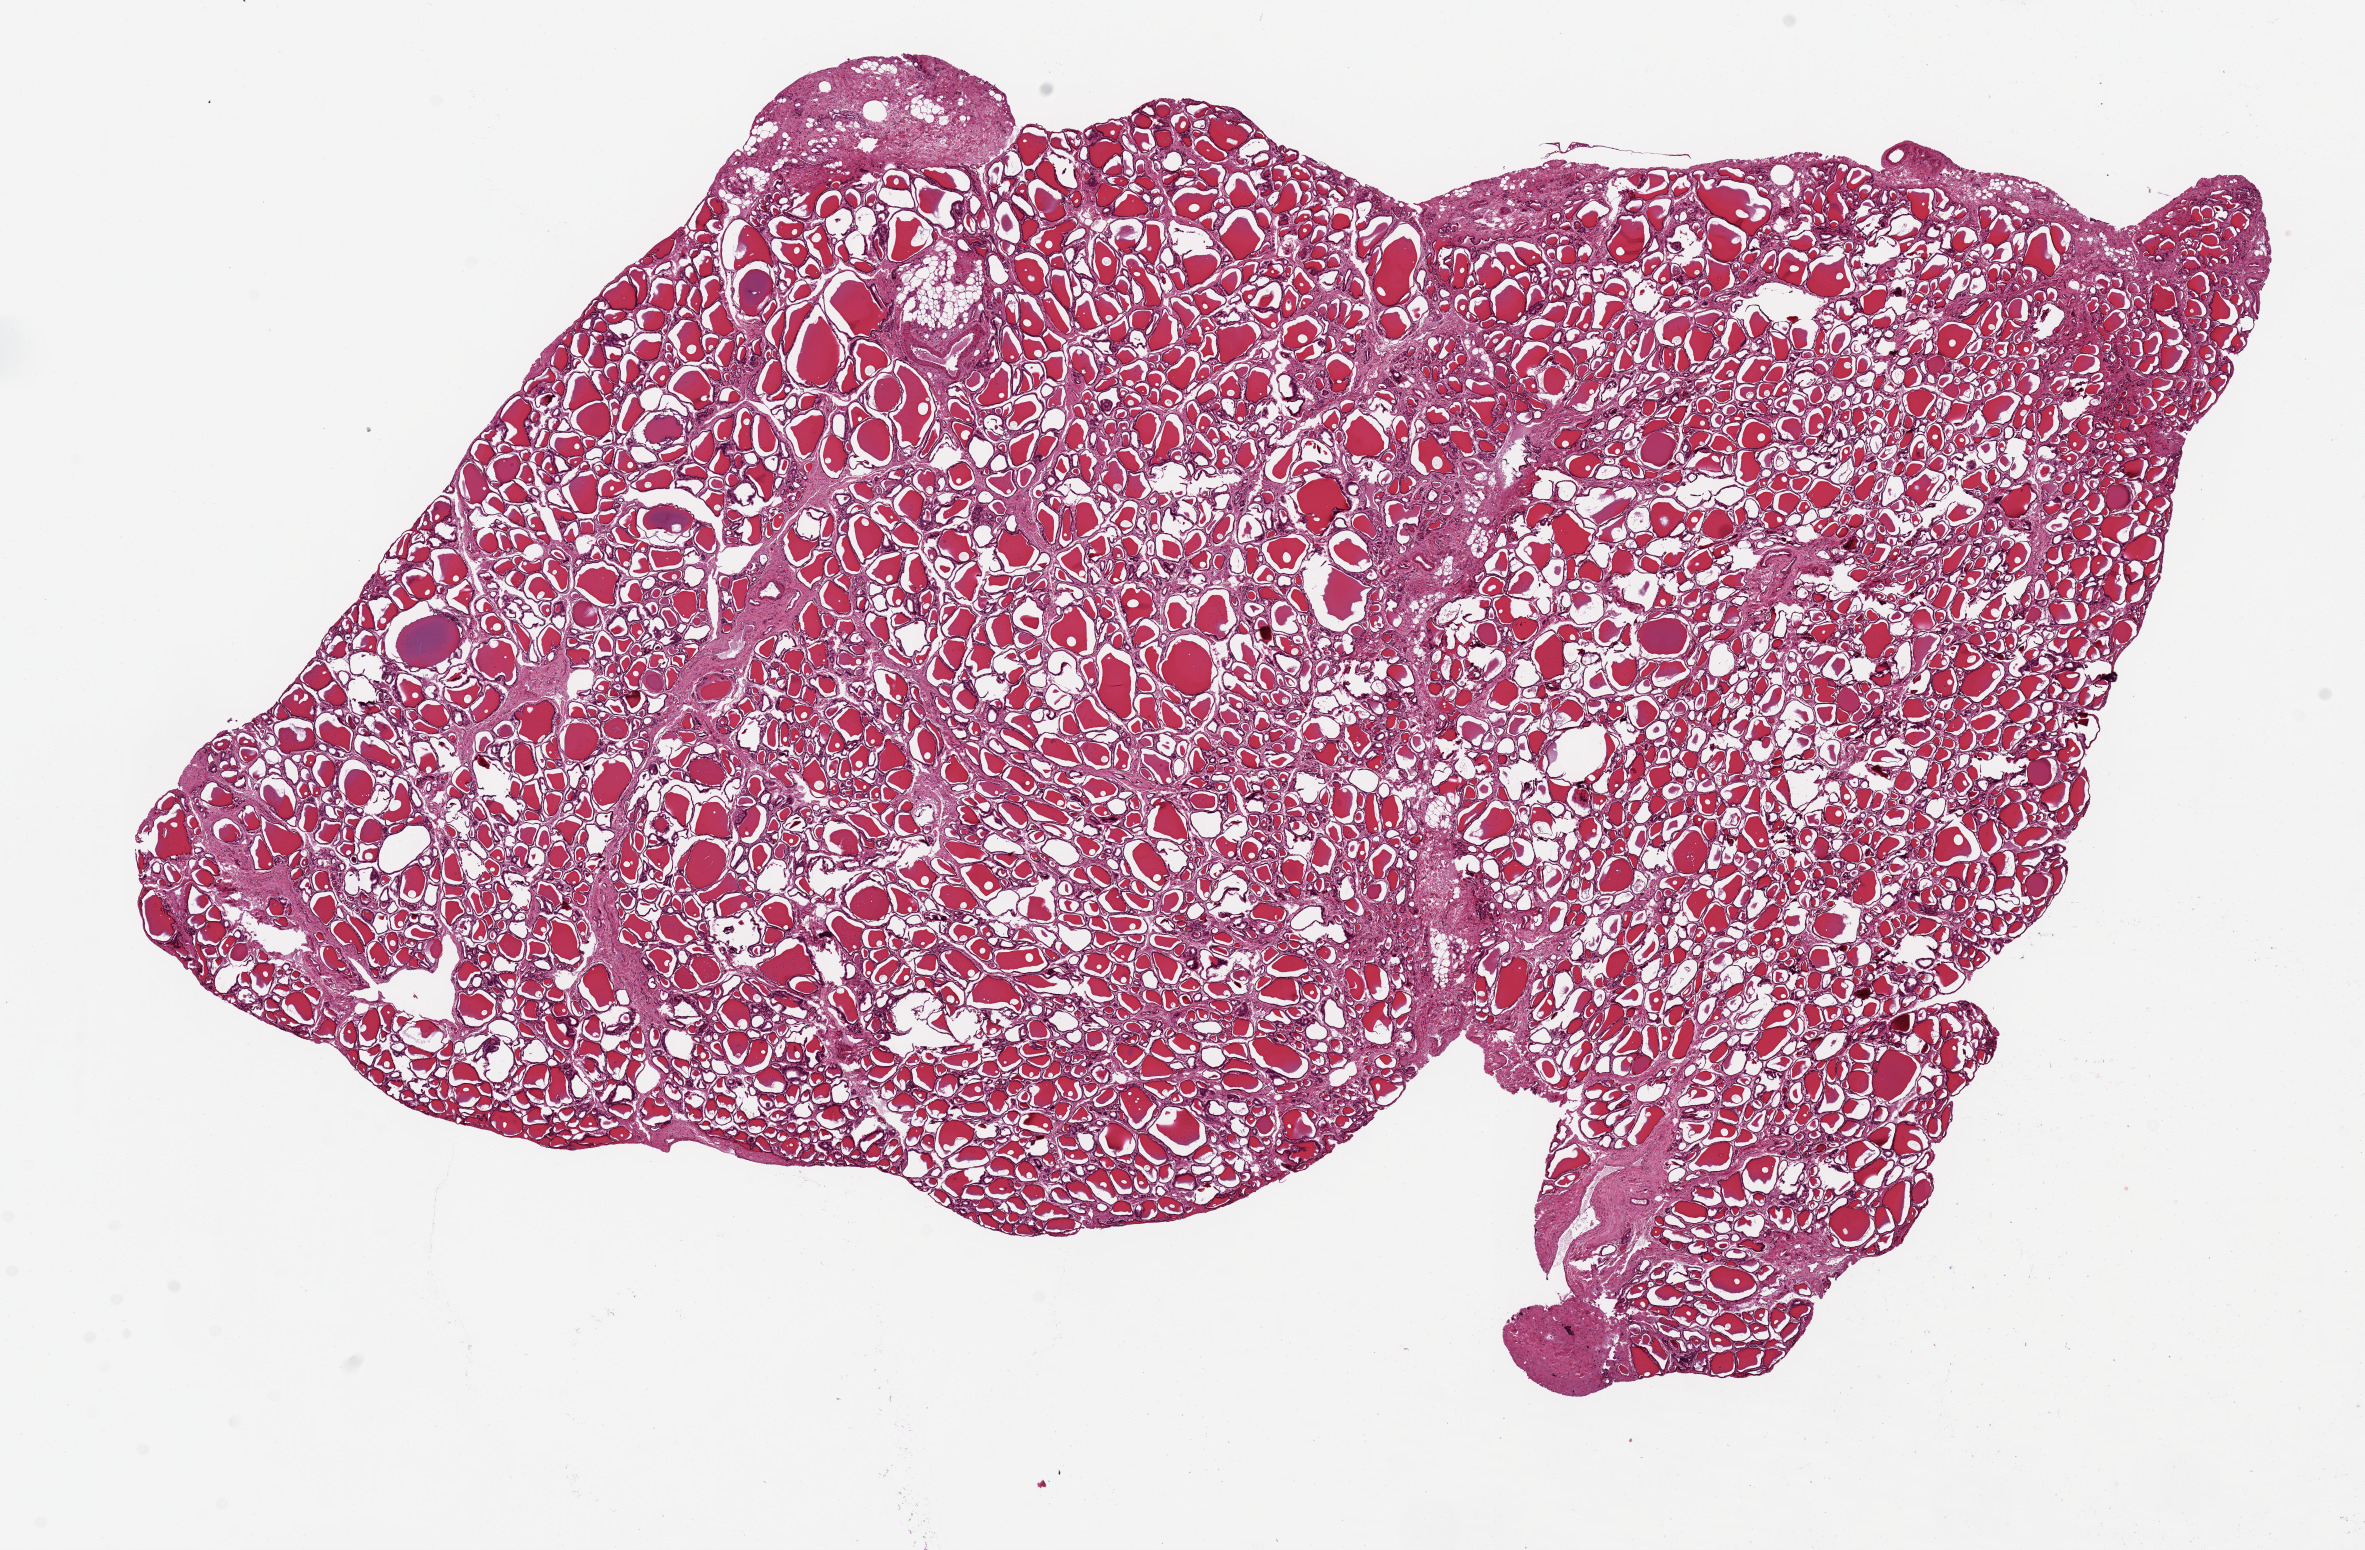
Whole-slide image, H&E stain, shown as a low-resolution overview of the whole scanned area (about 18.7 x 12.3 mm), PAXgene-fixed paraffin-embedded (PFPE) section, sampled site (target tissue): thyroid, donor tissue sample. Female donor.
• review note (as recorded): 1 ~14x7mm aliquot, no visible goiter